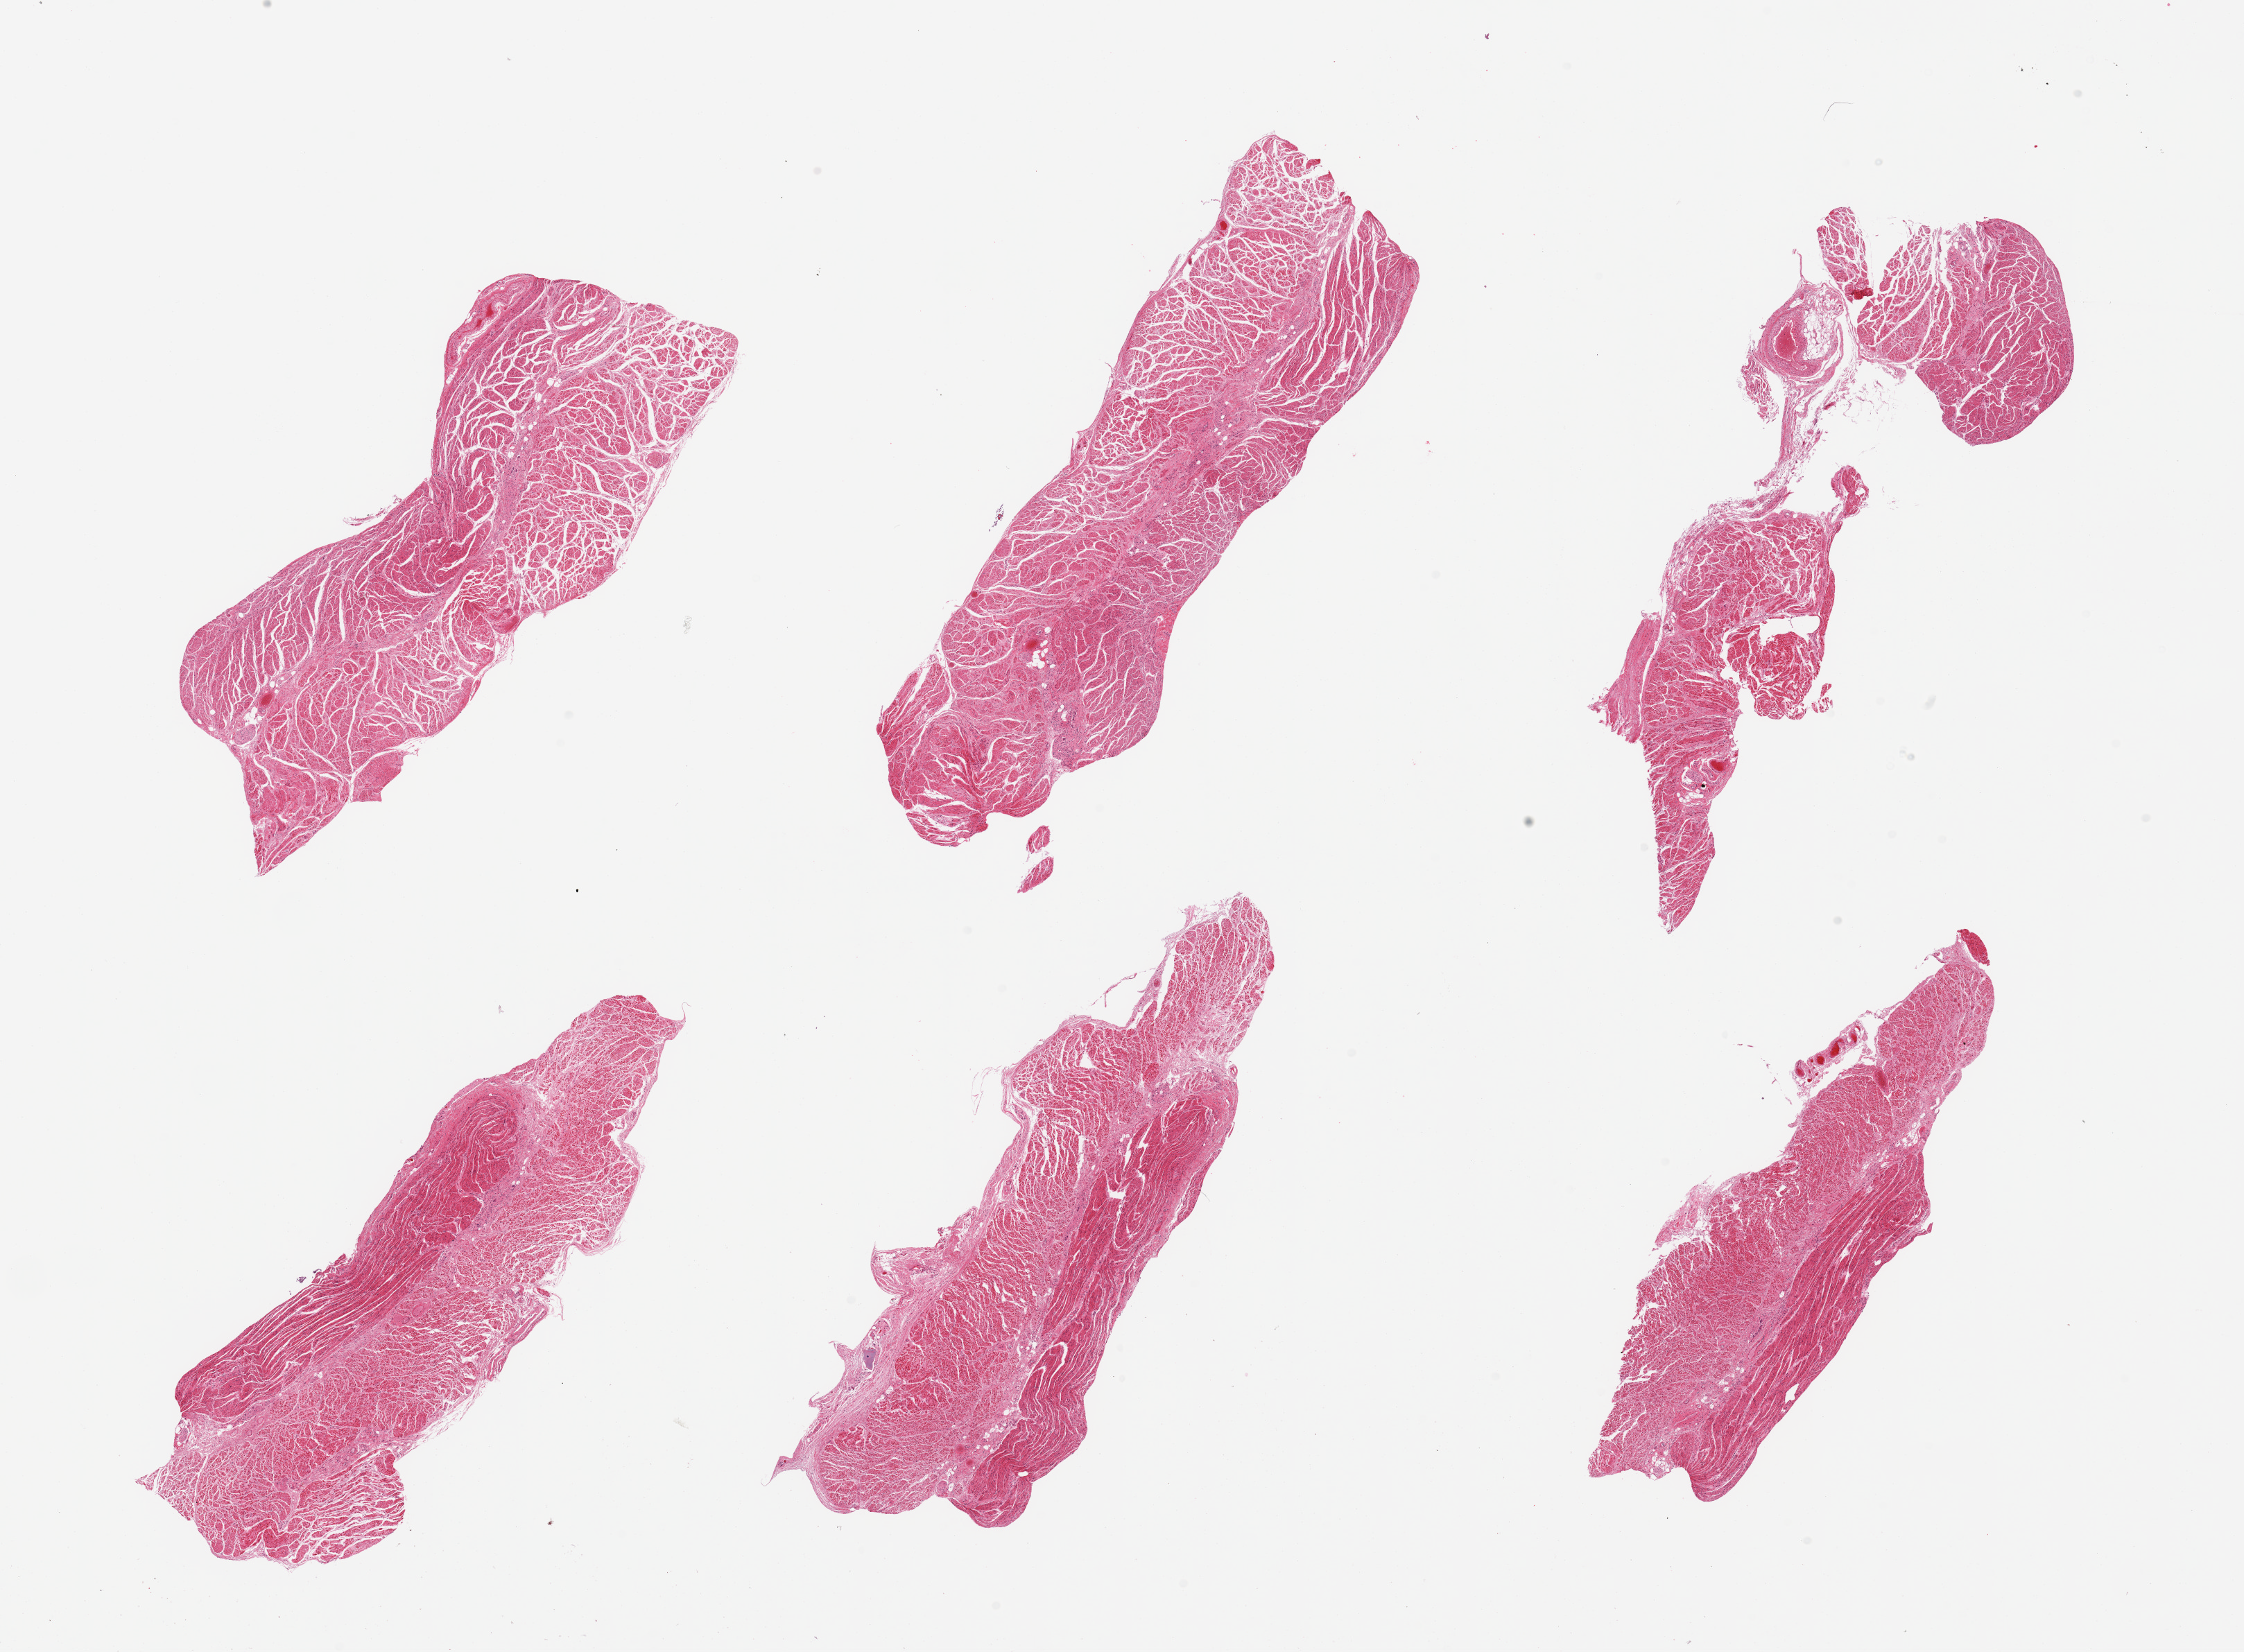
H&E whole-slide image, brightfield — low-resolution overview of the scanned area, about 25.6 x 18.8 mm (slide scanned at 20x); PAXgene-fixed paraffin-embedded (PFPE) section; sampled site (target tissue): gastroesophageal junction; donor tissue sample. Donor: male.
• pathologist's review note for this sample: 6 pieces; well dissected muscle